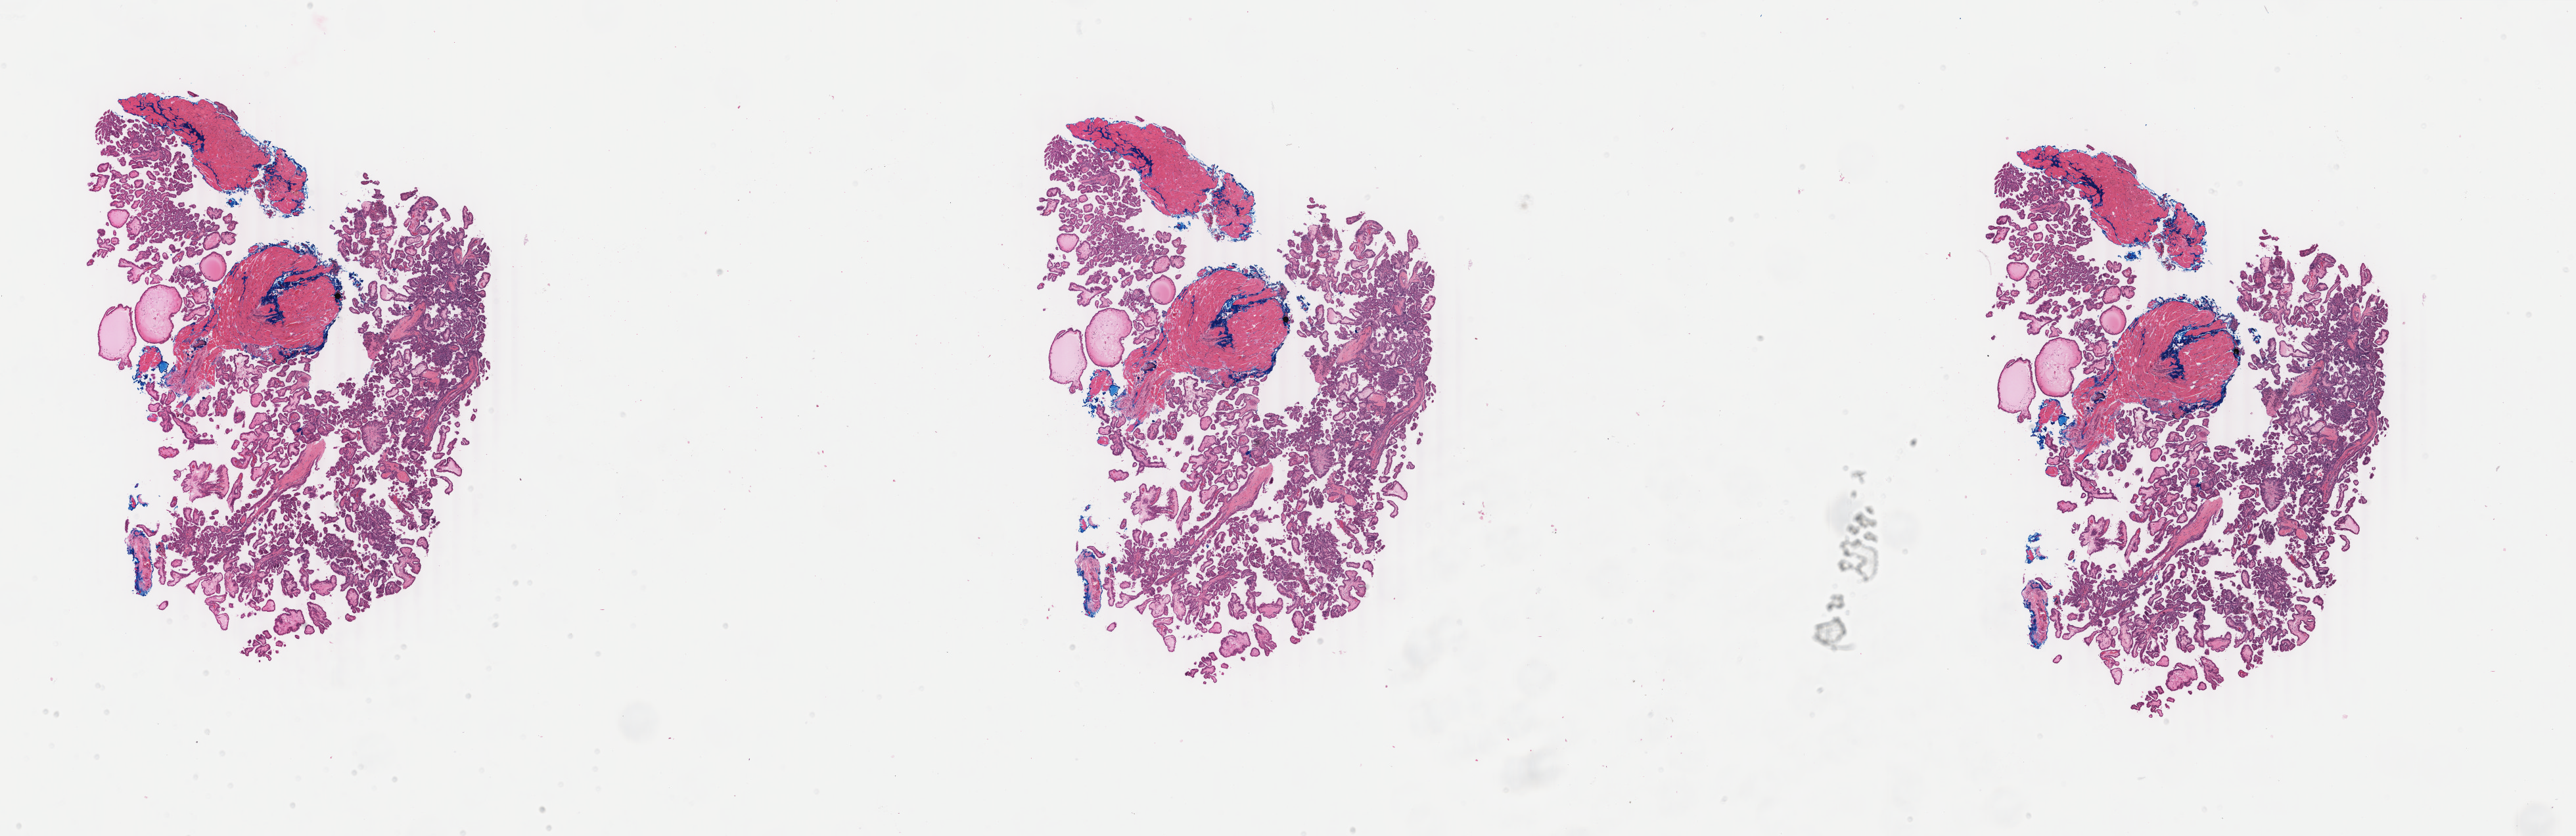
Whole-slide histology image, H&E — low-resolution overview of the scanned area, about 31.2 x 10.1 mm (acquisition: 40x scan), formalin-fixed paraffin-embedded (FFPE) diagnostic section, sample: primary tumour, thyroid. Patient: female, age at initial diagnosis 30 years.
Diagnosis: Papillary adenocarcinoma, NOS (thyroid gland). AJCC pathologic stage: I. Lymph nodes positive (case pathology): 6 of 11 examined. TNM: T2 N1a M0.